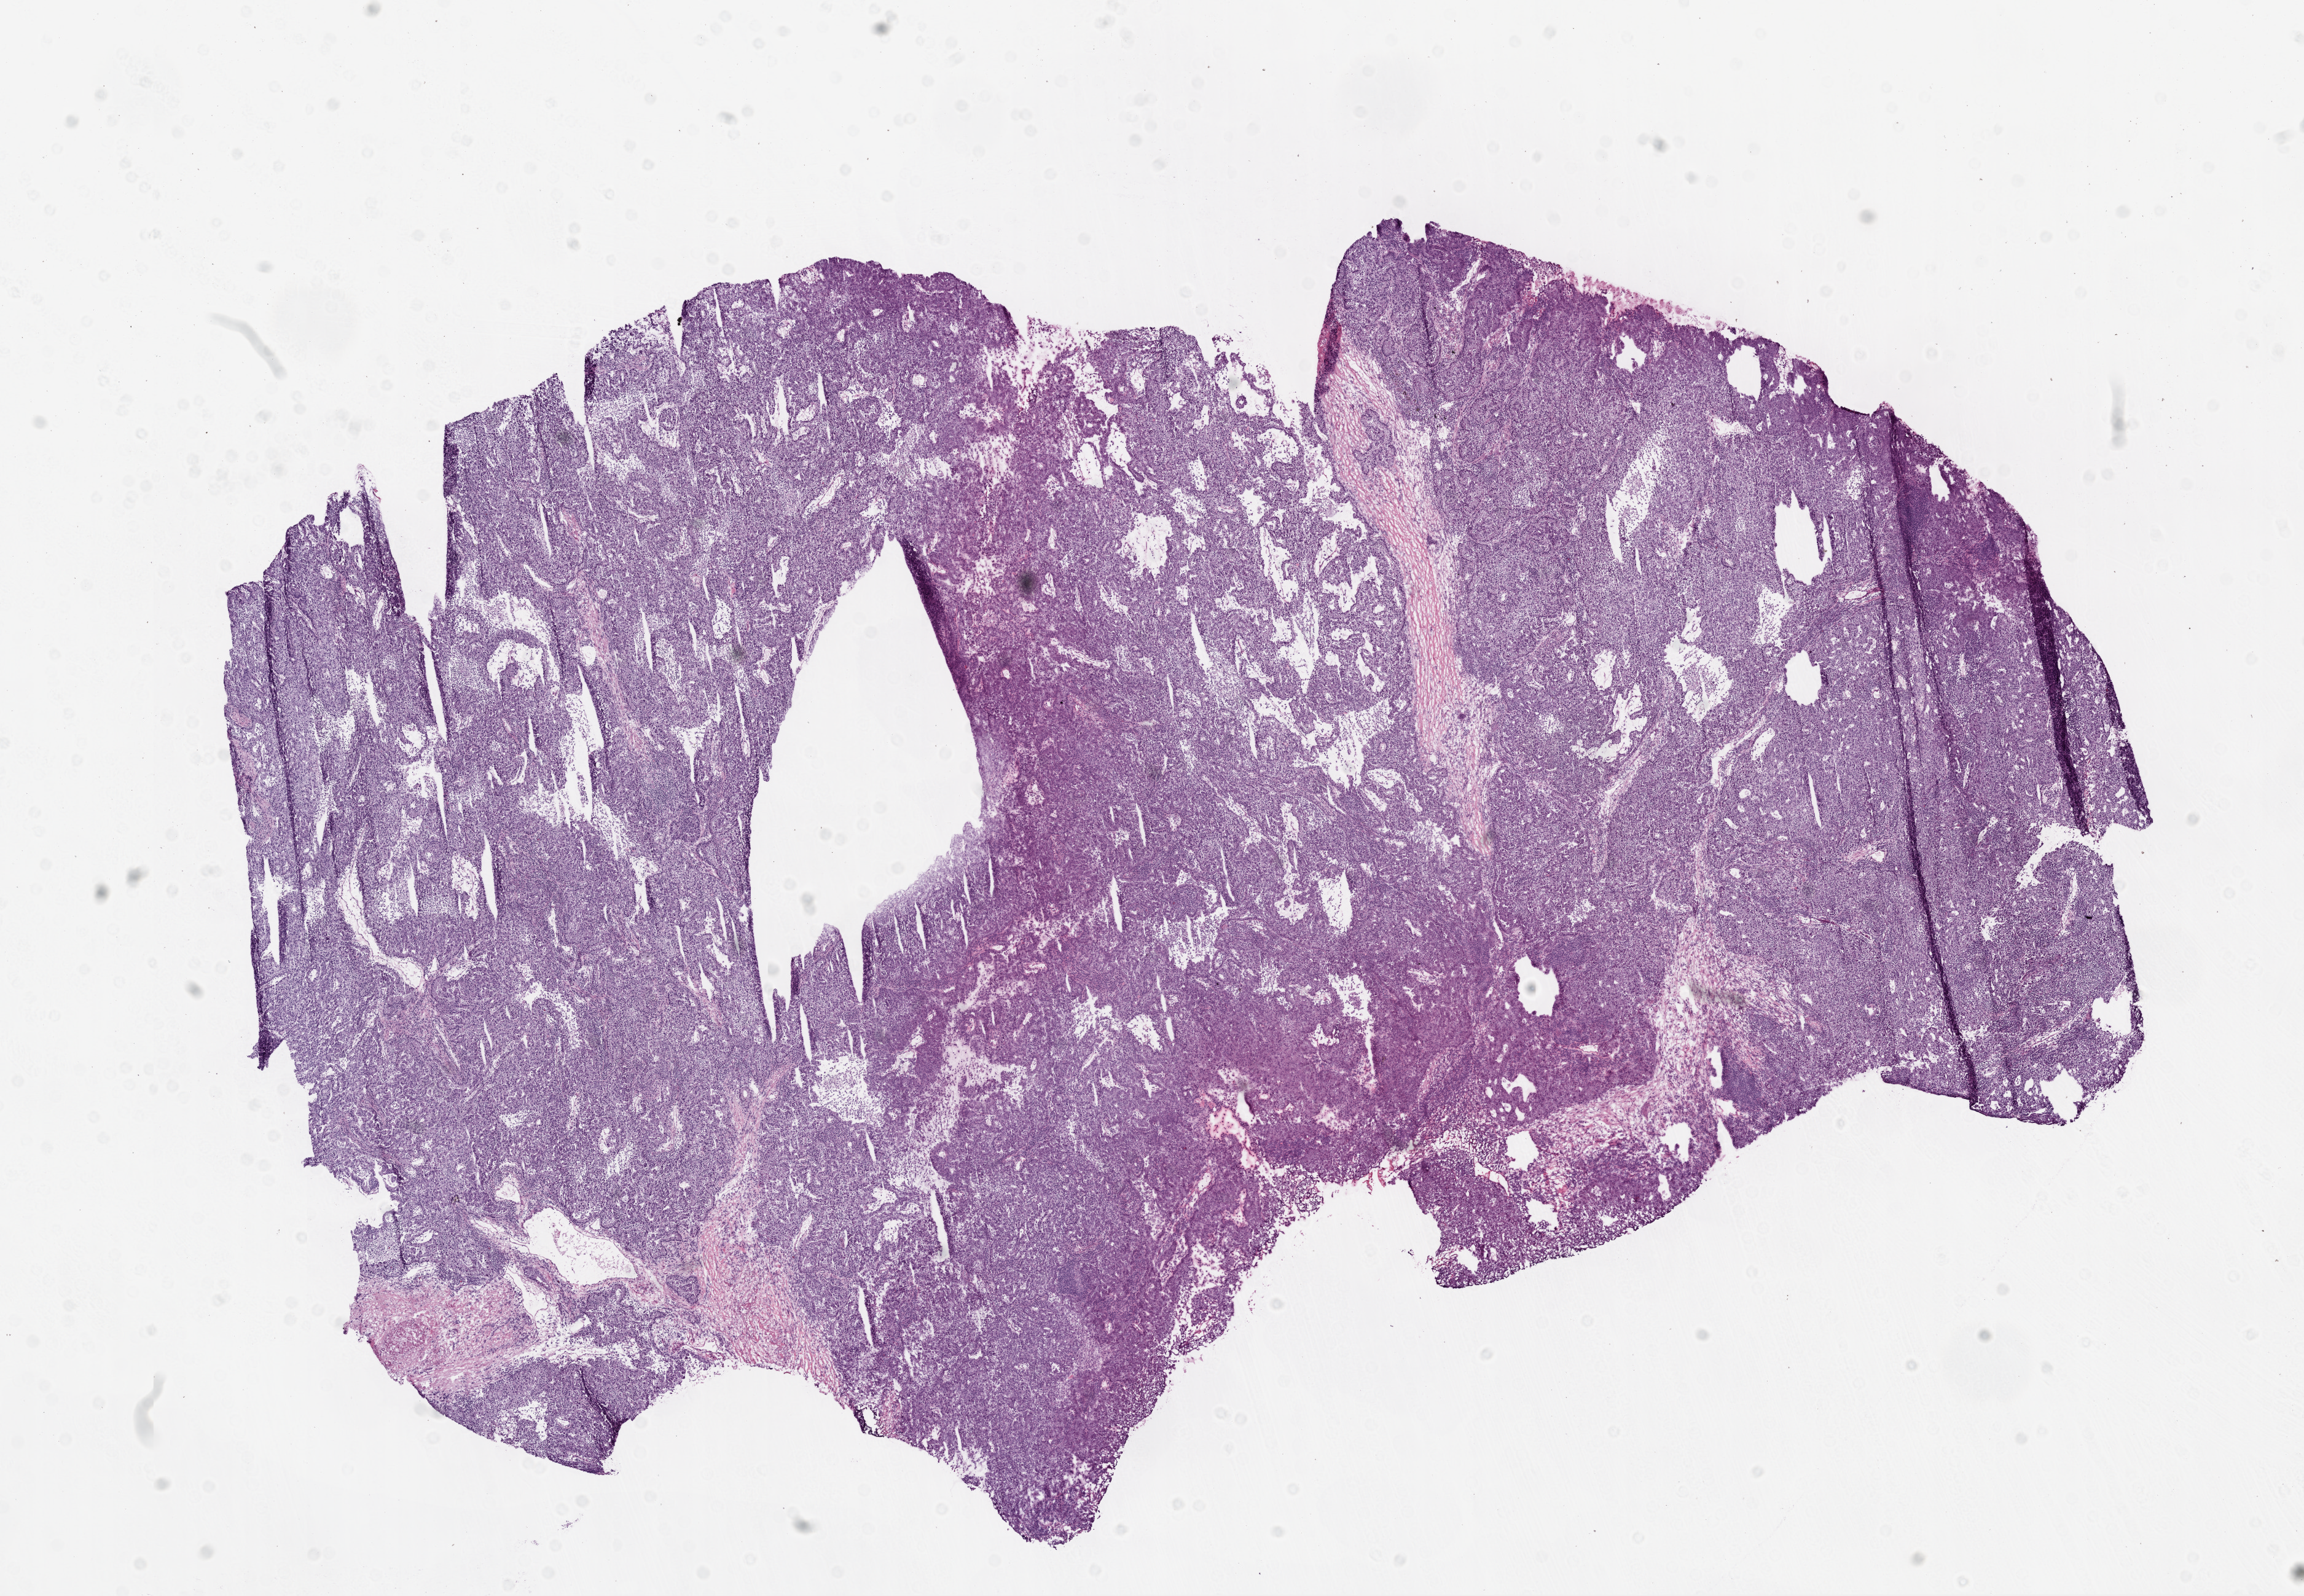
Digitized H&E-stained tissue section (whole slide) — whole scanned area (about 15.0 x 10.4 mm) shown as a low-resolution overview, frozen section from the bottom of the tissue portion, lung, primary tumour sample. Male, age 68 years at initial diagnosis. Slide review estimates, as recorded: tumour cells 89%, tumour nuclei 70%.
Diagnosis: Adenocarcinoma with mixed subtypes.